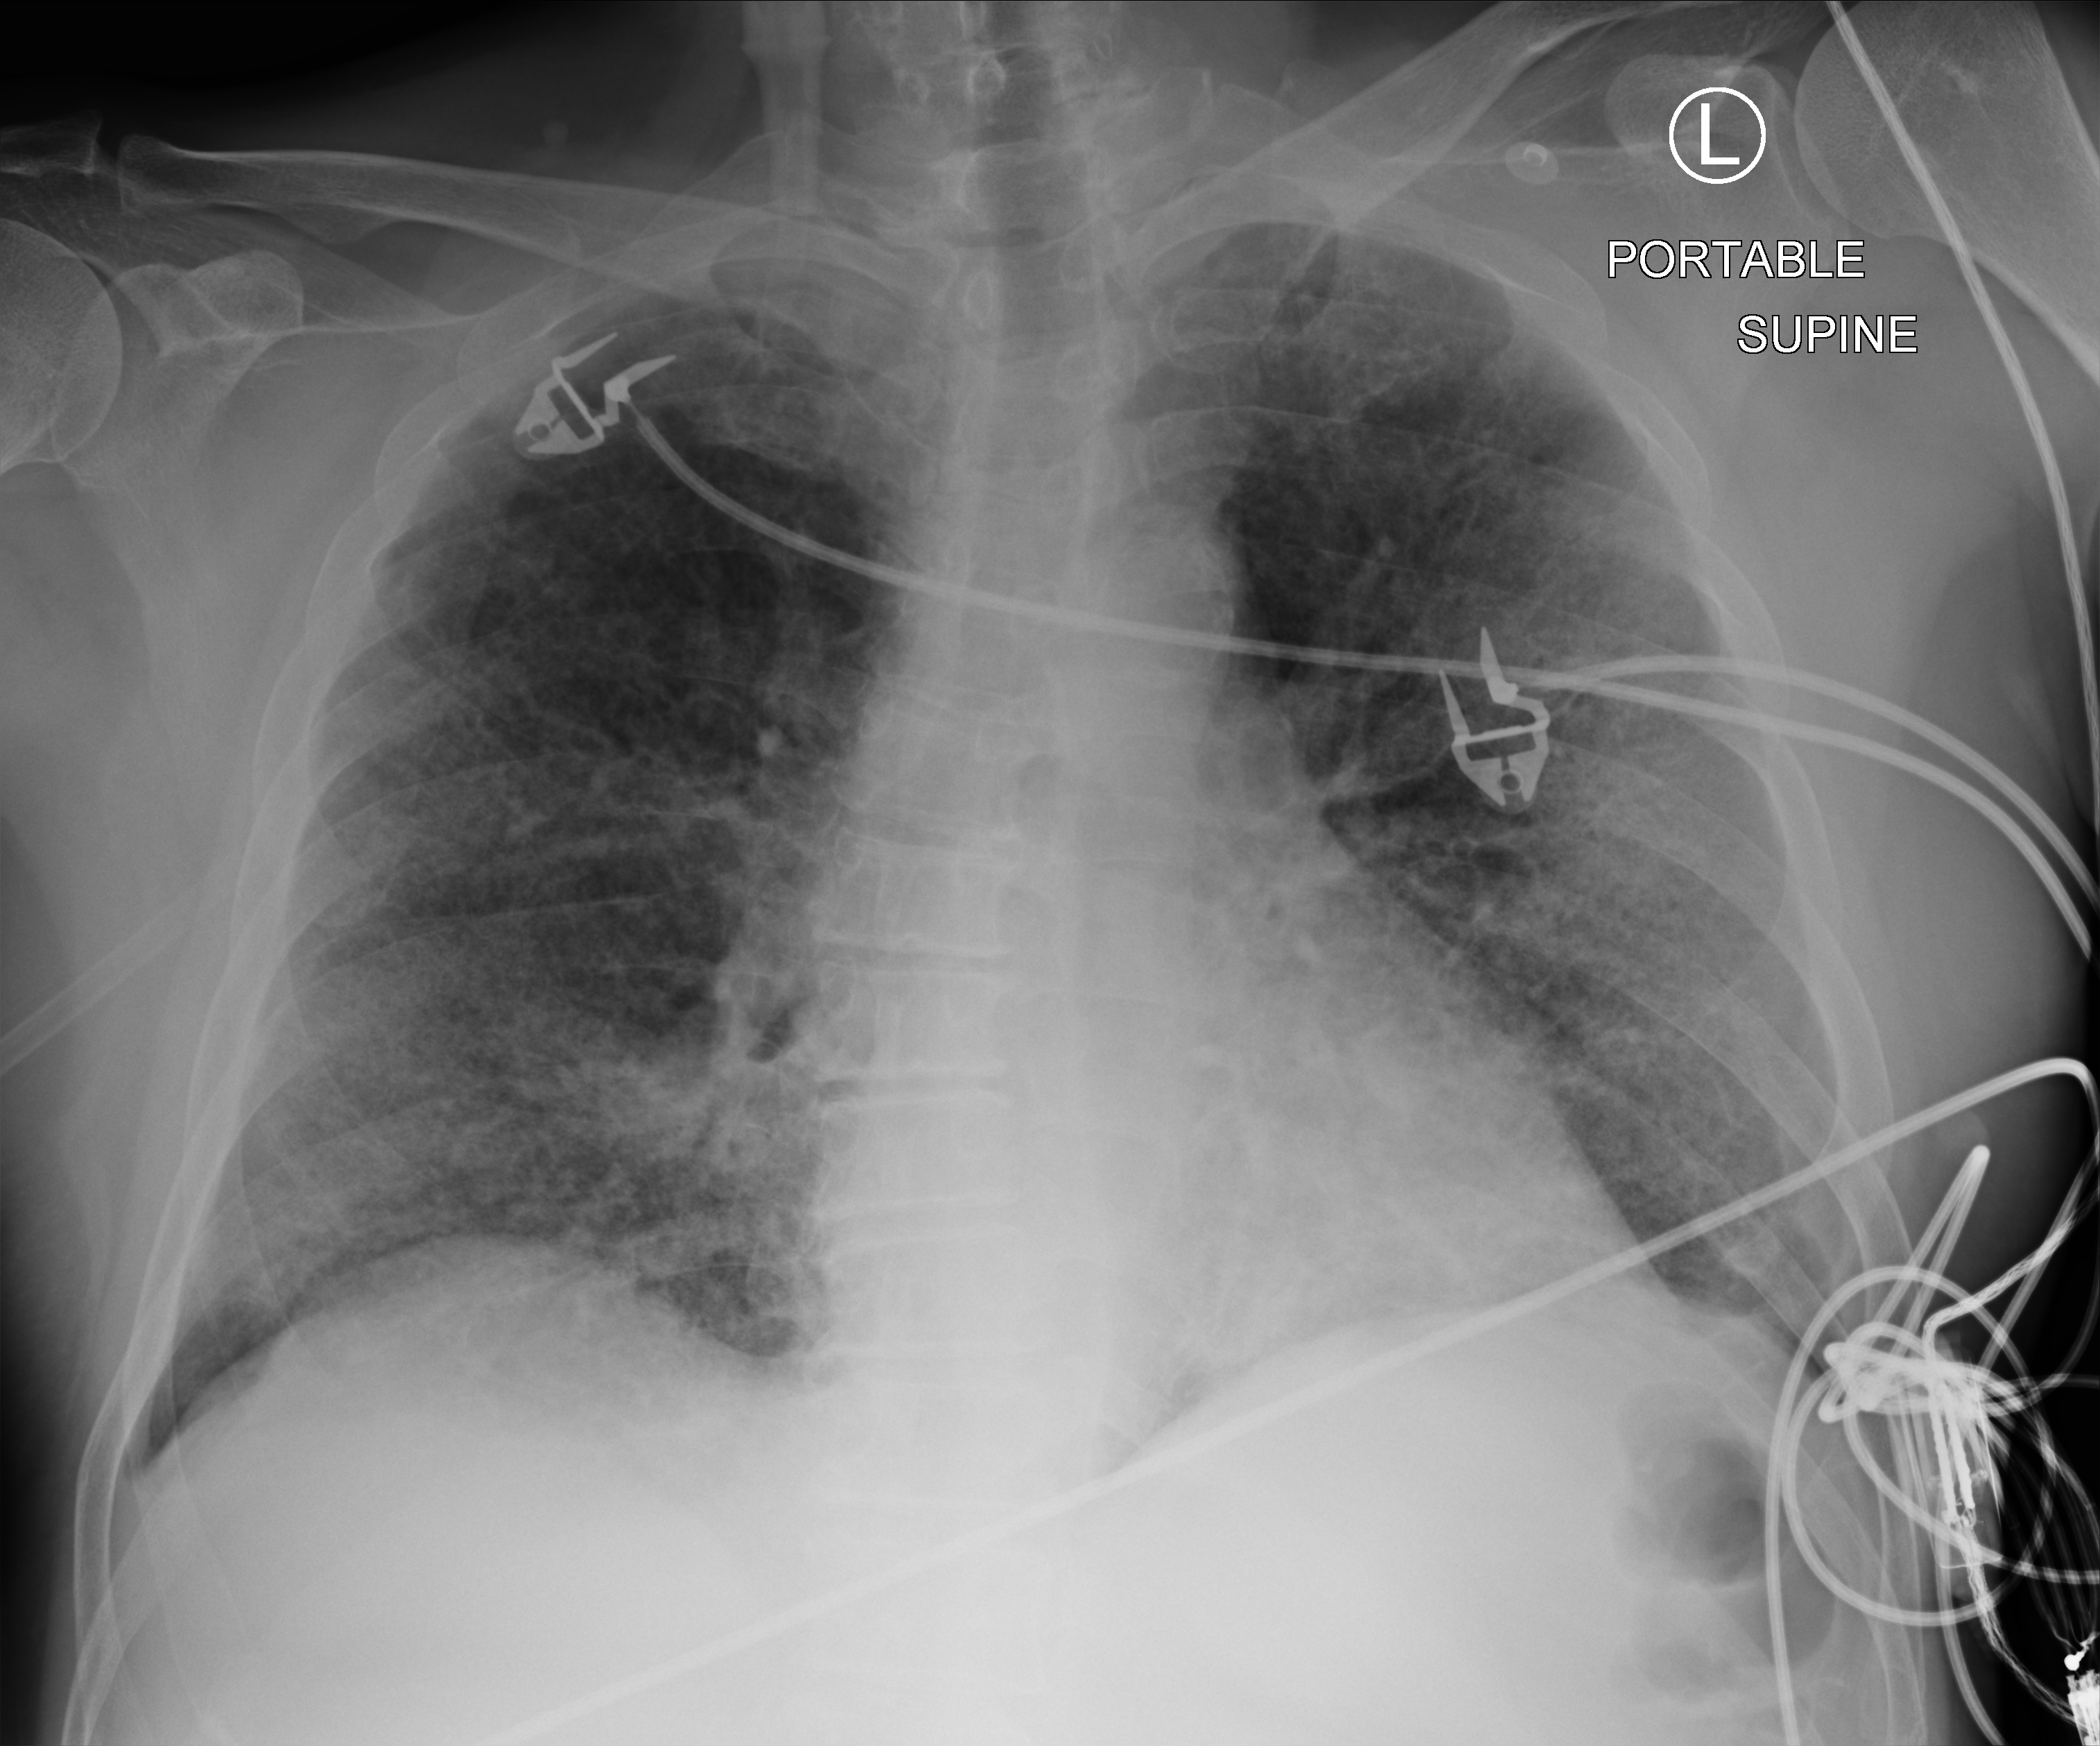
Portable chest radiograph; anteroposterior (AP) projection. Male patient hospitalised with COVID-19, age 18–59 years.
From the hospital-stay record, not from the radiograph (when in the stay this image was taken is not recorded):
- length of hospital stay: 18 days
- admitted to intensive care during this hospital stay: no